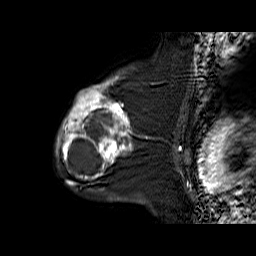
Breast MRI (dynamic contrast-enhanced), one sagittal slice. Slice 46 of 60 in the series (ordered by position). Dynamic contrast-enhanced series, time point 2 of 6 at this slice position (early post-contrast). 1.5 T. TE 6.3 ms, TR 32.9 ms. 256 × 256 image matrix, field of view 200 × 200 mm. Female patient. From the clinical record (not read from this slice): setting: breast cancer imaged before/during neoadjuvant chemotherapy; receptor status: triple-negative.
Structures marked on this image (semi-automatically segmented with operator editing):
- analysis volume of interest (the breast-tissue region the enhancement analysis was run in; not a lesion): bounding box [x1, y1, x2, y2] px = [56, 76, 144, 170]
- tumour enhancement mask (voxels above the 100 % enhancement threshold inside the analysis volume of interest): [56, 76, 133, 169]